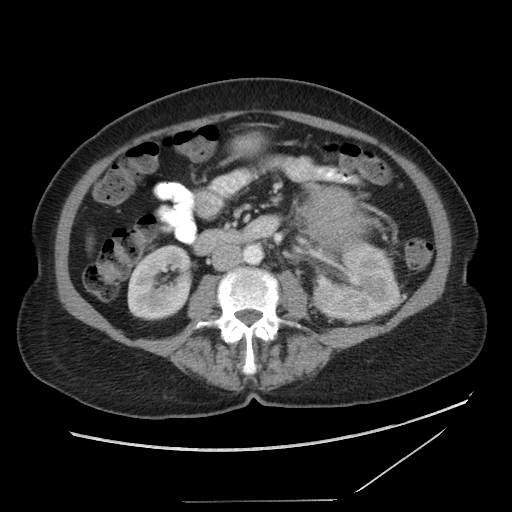
Contrast-enhanced abdominal CT, one axial slice. Slice 42 of 86 in the series (ordered by position). Reconstruction kernel STANDARD. 120 kVp. Soft-tissue window (W 400 / L 40 HU). 5 mm slice thickness. 512 × 512 image matrix, field of view 398 × 398 mm. Patient: female, 77 years. Case-level facts recorded for this patient, not image findings: diagnosis: adrenocortical carcinoma; tumour side: left adrenal; tumour size at pathology: 13.1 cm; Ki-67 index: 10 %; stage (as recorded): 3.
Outlined on this slice (semi-automatically segmented with operator editing):
- mass: bounding box (x1, y1, x2, y2) in pixels: (306, 189, 361, 252)